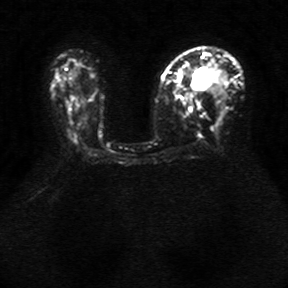
Breast MRI, one axial slice; position 17 of 34 along the scan axis; diffusion-weighted series; image 2 of 4 stored at this slice position (different b-values; order by instance number); 1.5 T; 5 mm slice thickness; 288 × 288 image matrix, field of view 340 × 340 mm. Female patient.
Structures marked on this image (outlined manually by an expert reader):
- tumour on diffusion-weighted imaging: bounding box (x1, y1, x2, y2) in pixels: (193, 70, 212, 88)